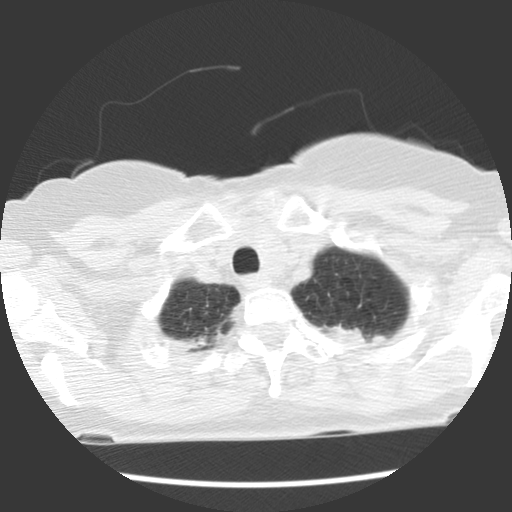
Chest CT (low-dose screening protocol), one axial image. Baseline screening round. Lung window (W 1500 / L -600 HU). 2.5 mm slice thickness. Standard (soft-tissue) reconstruction kernel (STANDARD). Slice 105 of 120 in the series. 512 × 512 image matrix. Female participant, aged 66 years at enrolment. Former smoker at enrolment.
Expert-annotated lung lesion, bounding box [x1, y1, x2, y2] px = [315, 300, 385, 358]. Reader record for this screening exam (exam-level; its link to the box is not recorded): non-calcified nodule or mass ≥4 mm, left upper lobe, 22 × 17 mm, spiculated (stellate) margins, soft tissue attenuation. Official screen result: positive, change unspecified: nodule(s) >= 4 mm or enlarging nodule(s), mass(es), or other non-specific abnormalities suspicious for lung cancer. Later outcome: lung cancer diagnosed 50 days after this screen — adenocarcinoma, NOS, left upper lobe, poorly differentiated (G3), stage IB (AJCC 6th edition), 40 mm at pathology.